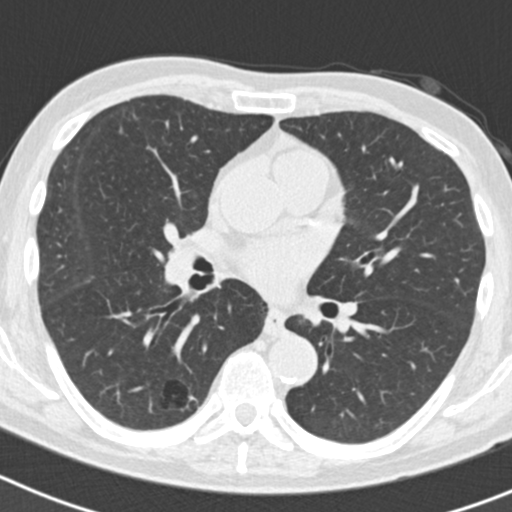
Axial slice from a low-dose chest CT screening exam. Second screening round (one year after baseline). Lung window (W 1500 / L -600 HU). 120 kVp. Slice 84 of 186 in the series. Male participant, aged 70 years at enrolment. Current smoker at enrolment.
Lesion marked by an expert reader, box from (x=129, y=368) to (x=201, y=431) px. The screening reader recorded 5 non-calcified nodules or masses ≥4 mm on this exam (right lower lobe, right lower lobe, right upper lobe, right upper lobe, left upper lobe); which of them this box marks is not recorded. Lung cancer was diagnosed 622 days after this screen: bronchiolo-alveolar adenocarcinoma, NOS, right lower lobe, poorly differentiated (G3), stage IB (AJCC 6th edition), 30 mm at pathology.